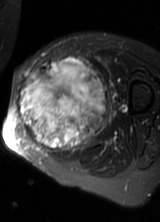
MRI of an extremity soft-tissue mass, one axial slice. T2-weighted fat-saturated. MR volume resampled by the dataset authors to the PET/CT grid (not the native acquisition matrix). 160 × 222 image matrix, field of view 156 × 217 mm. Female patient. From the clinical record (not read from this slice): histological type: pleomorphic leiomyosarcoma; grade: high; site of the primary tumour: left thigh.
Outlined on this slice (expert contour drawn on MRI and transferred to this co-registered scan by the dataset authors):
- gross tumour volume including surrounding oedema: bounding box <16,56,108,153> (left, top, right, bottom; pixels)
- gross tumour volume (mass): <16,59,106,151>